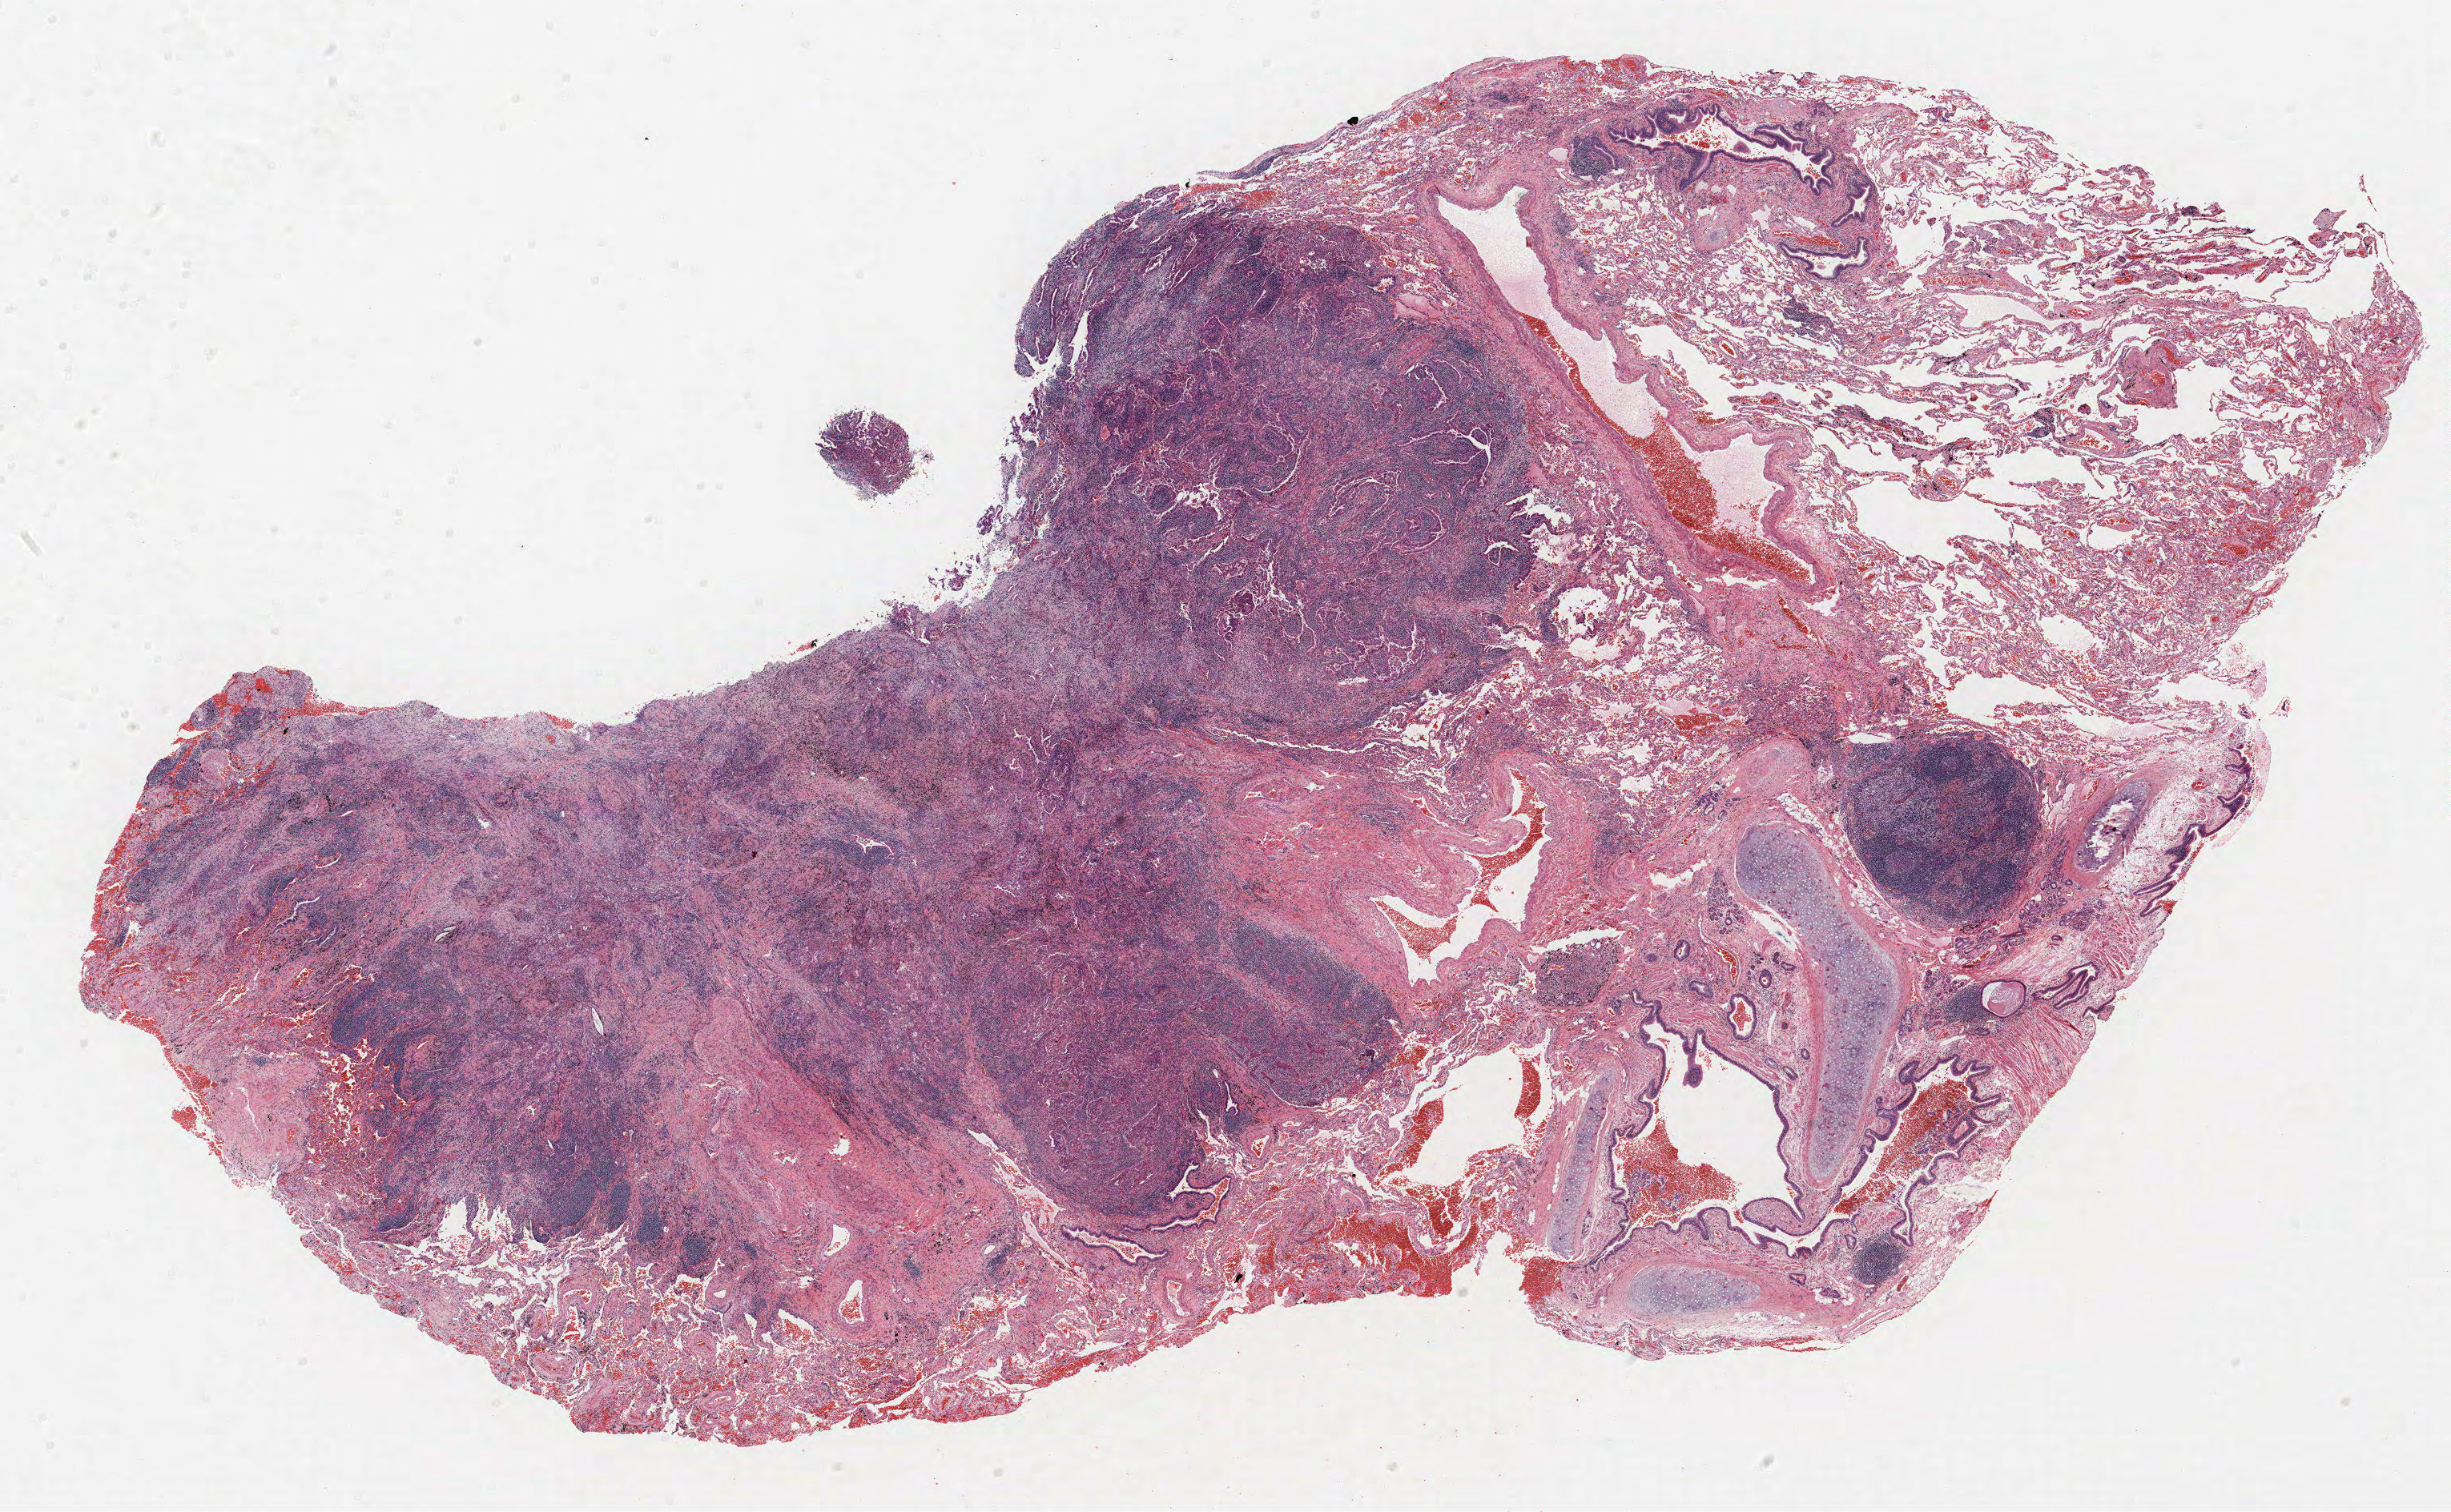
H&E whole-slide image, a low-resolution overview of the entire scanned area, about 24.5 x 15.1 mm (acquisition: 40x scan). FFPE section. Lung tissue. Female, age 67 at enrolment. Former smoker at enrolment. Grade: moderately differentiated (G2).
- tumour size (pathology): 14 mm
- participant's lung-cancer diagnosis: Adenocarcinoma, NOS
- stage (AJCC 6th edition): IA
- primary tumour location (clinical record): right upper lobe